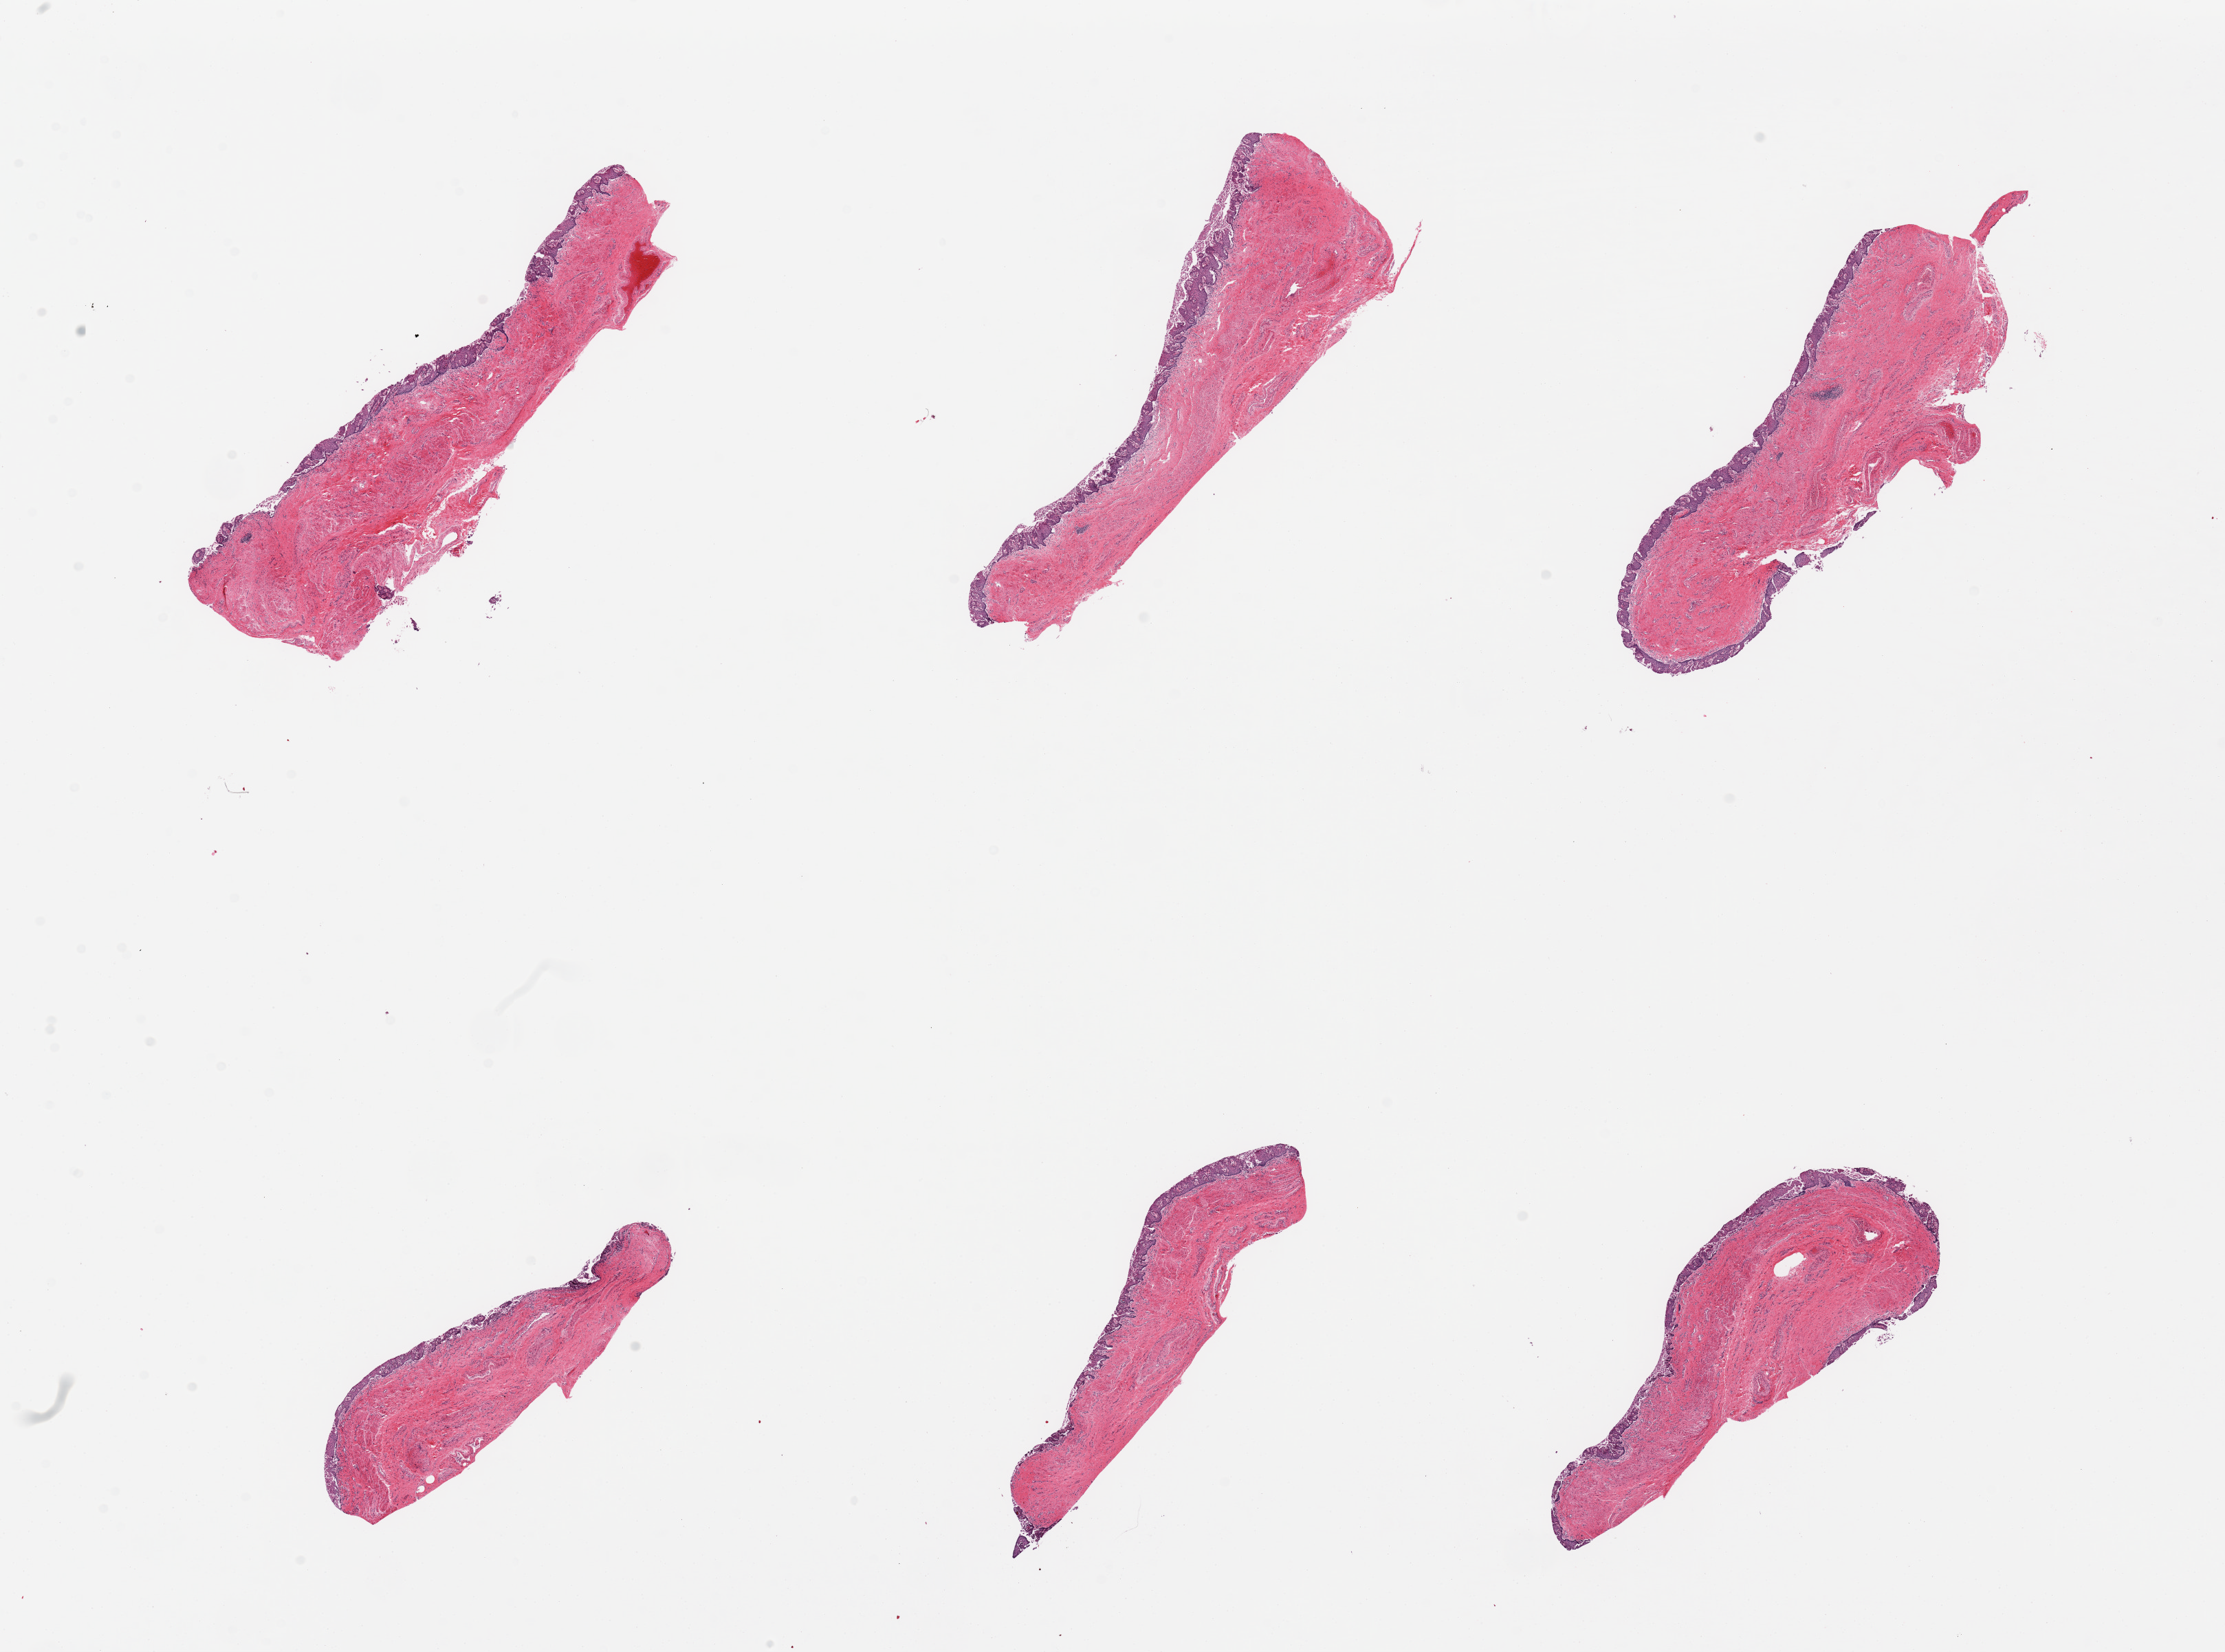
Hematoxylin and eosin (H&E) whole-slide image, brightfield — whole scanned area (about 25.6 x 19.0 mm) shown as a low-resolution overview. PAXgene-fixed paraffin-embedded (PFPE) section. Target tissue: esophageal mucous membrane. Tissue donor sample. Donor sex: male.
Pathologist's review note for this sample: 6 pieces, squamous mucosa is ~10% thickness, sloughing/ autolyzing.